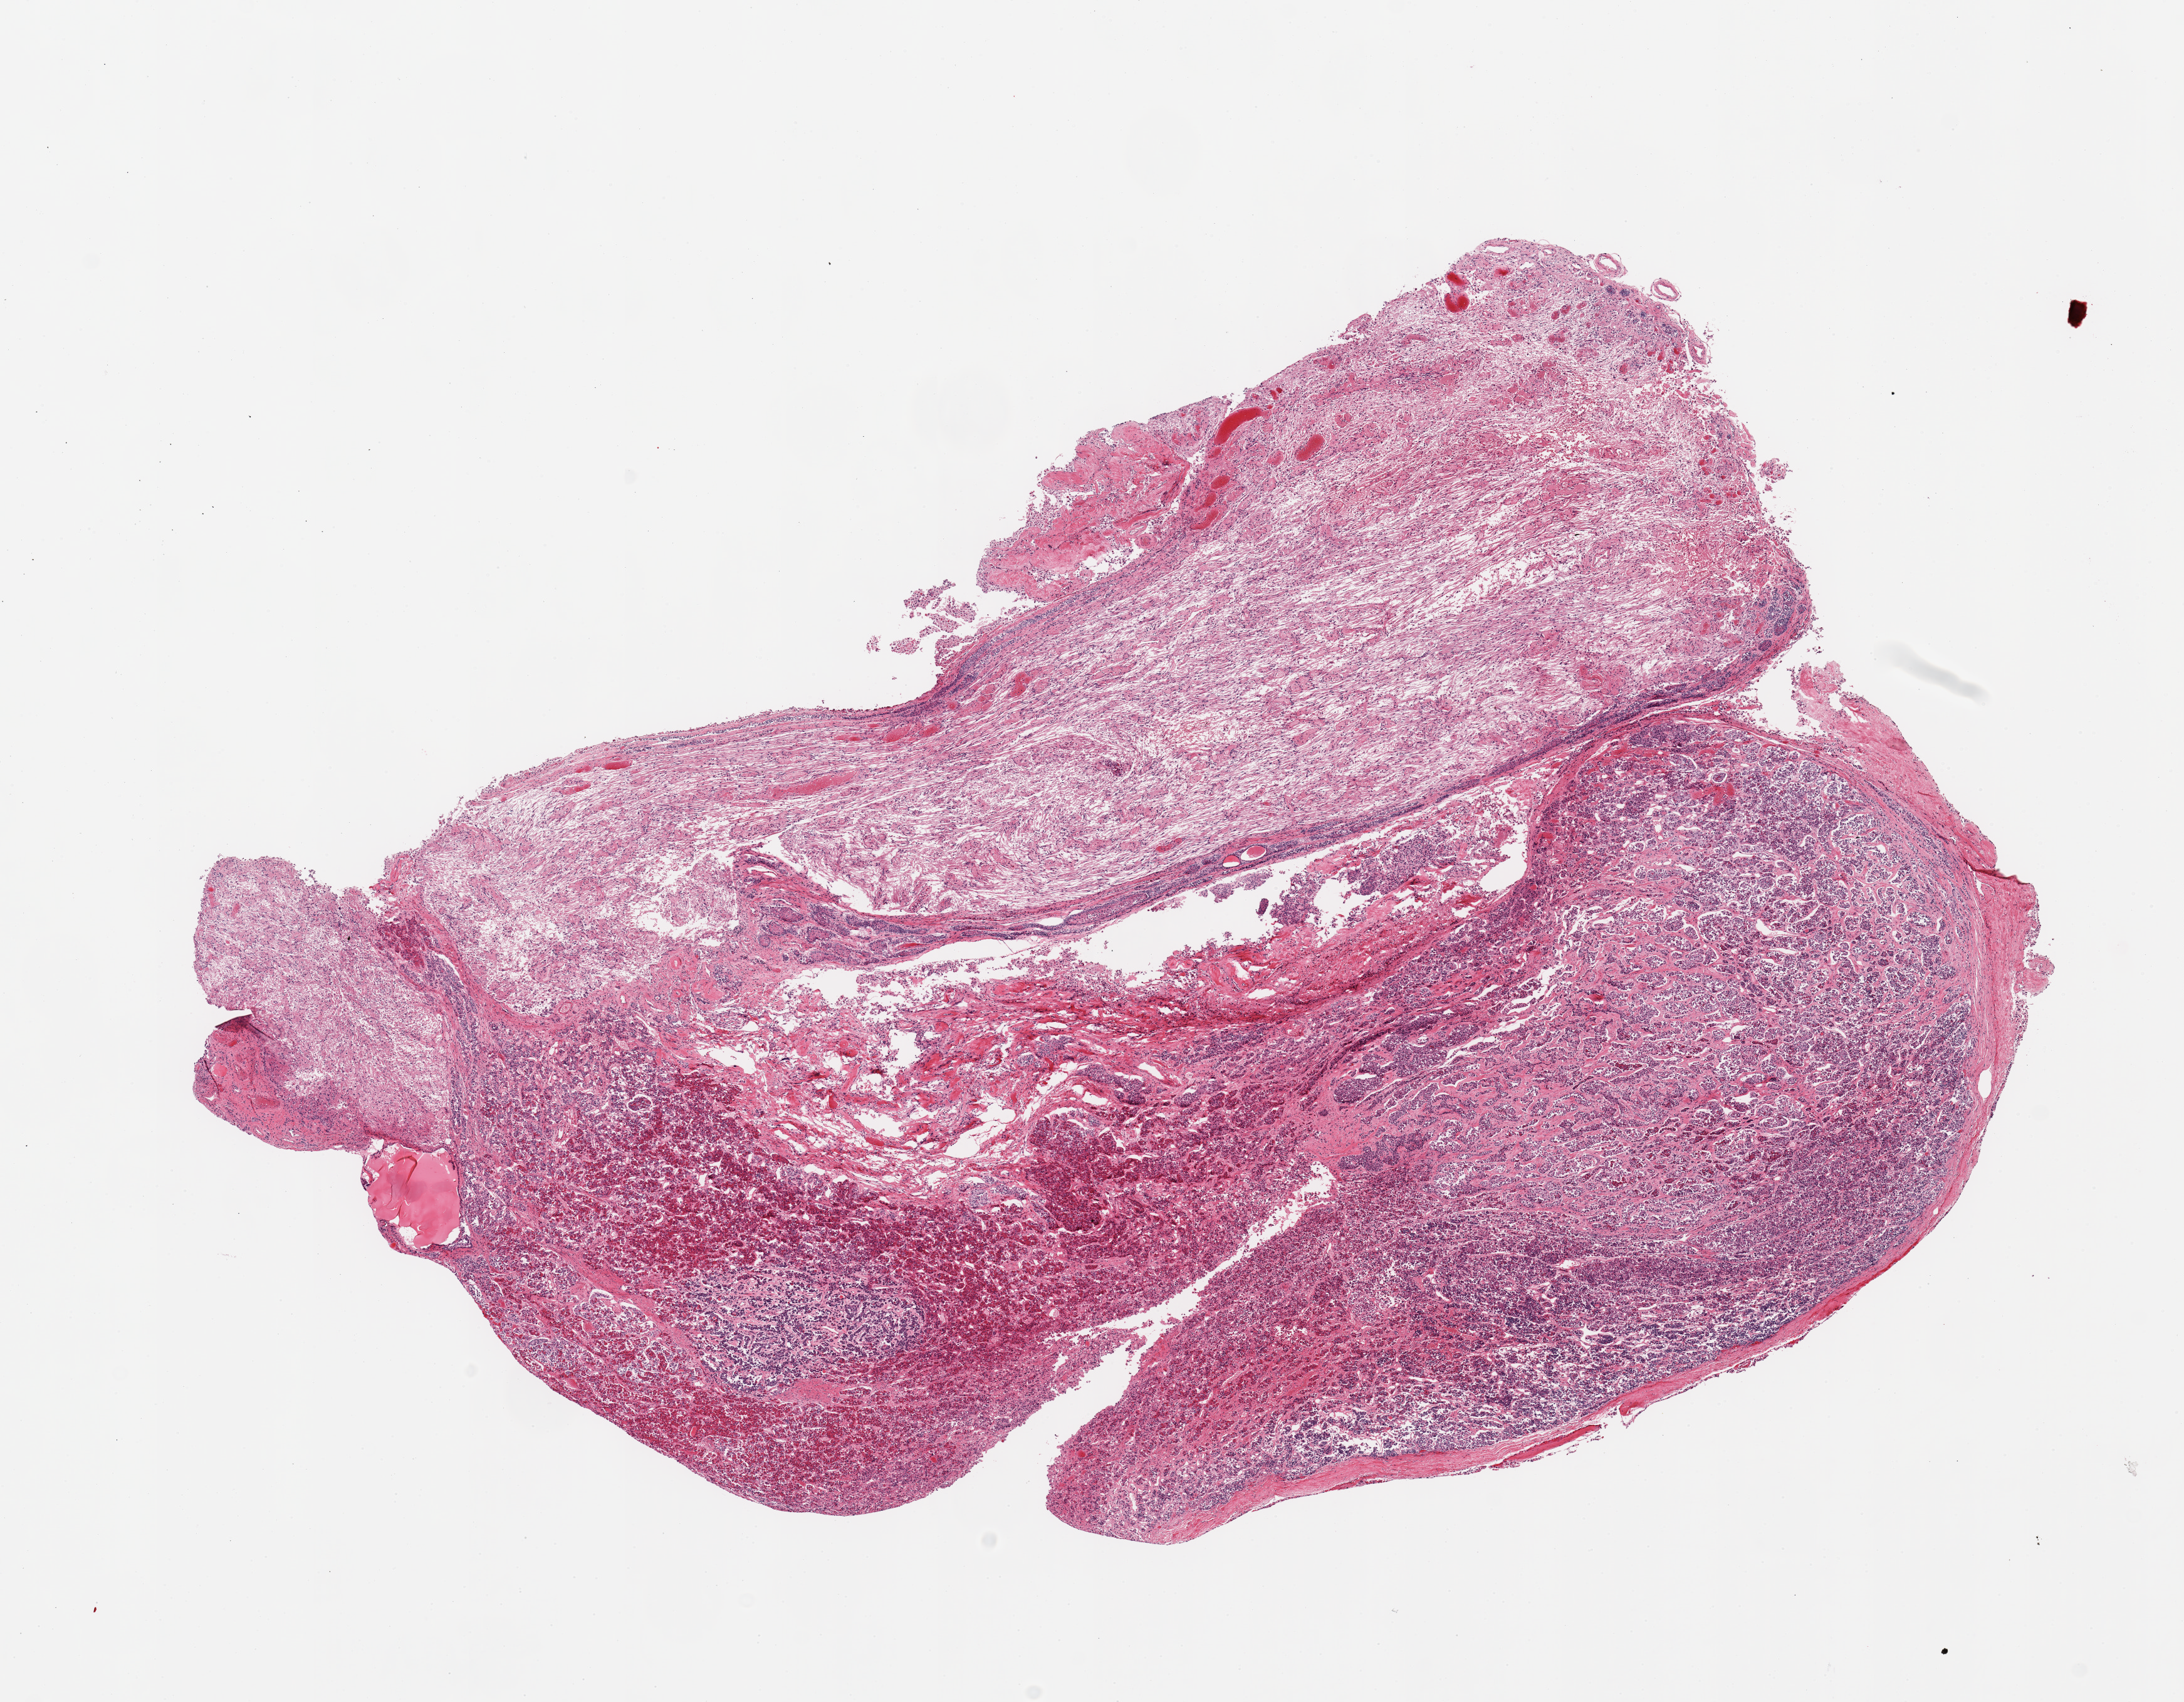
Whole-slide image, haematoxylin and eosin stain — shown as a low-resolution overview of the whole scanned area (about 13.8 x 10.7 mm, from a 20x scan), PAXgene-fixed paraffin-embedded (PFPE) section, section of pituitary (target tissue), donor tissue sample. Donor: male.
Review note (as recorded): 1 piece~ 40% neurohypophysis; rest adenohypophysis.